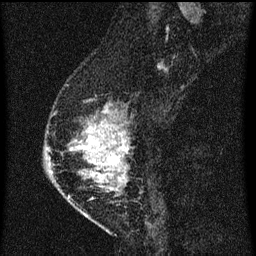
Breast MRI (dynamic contrast-enhanced), one sagittal slice; position 20 of 60 along the scan axis; dynamic contrast-enhanced series, image 2 of 3 at this slice position (ordered by acquisition); 1.5 T; TE 4.2 ms, TR 8 ms; 2 mm slice thickness; 256 × 256 image matrix, field of view 180 × 180 mm. Patient: female, 47 years.
Structures marked on this image (semi-automatically segmented with operator editing):
- analysis volume of interest (the breast-tissue region the enhancement analysis was run in; not a lesion): bounding box (x1, y1, x2, y2) in pixels: (50, 86, 139, 203)
- tumour enhancement mask (voxels above the 70 % enhancement threshold inside the analysis volume of interest): (69, 110, 130, 199)